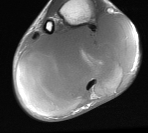
MRI of an extremity soft-tissue mass, one axial slice; slice 22 of 76 in the series (ordered by position); MR volume resampled by the dataset authors to the PET/CT grid (not the native acquisition matrix); 3.27 mm slice thickness; 148 × 133 image matrix, field of view 145 × 130 mm. Male patient. From the clinical record (not read from this slice): histological type: liposarcoma - round cell; grade: high; site of the primary tumour: right calf.
Annotated regions visible in this slice (expert contour drawn on MRI and transferred to this co-registered scan by the dataset authors):
- gross tumour volume (mass): bounding box [x1, y1, x2, y2] px = [15, 14, 139, 113]